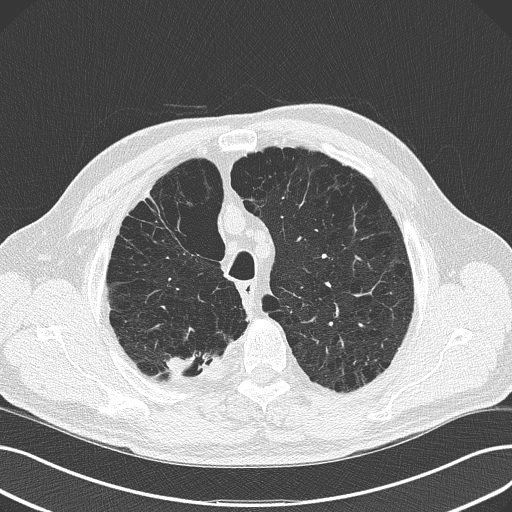
Low-dose screening chest CT, axial slice. Second screening round (one year after baseline). Lung window (W 1500 / L -600 HU). 2 mm slice thickness. Lung (sharp) reconstruction kernel (B50f). 512 × 512 image matrix. Male participant, aged 68 years at enrolment. Current smoker at enrolment.
Expert reader's lesion annotation, bounding box <143,333,227,395> (left, top, right, bottom; pixels). The screening reader recorded 4 non-calcified nodules or masses ≥4 mm on this exam (right upper lobe, left lower lobe, left upper lobe, right lower lobe); which of them this box marks is not recorded. Participant outcome: lung cancer diagnosed 304 days after this screen — adenocarcinoma, NOS, right upper lobe, stage IV (AJCC 6th edition), 29 mm at pathology.